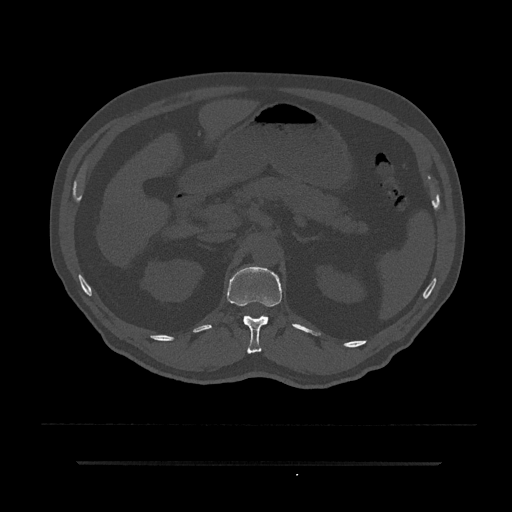
CT including the spine, one axial slice. Position 193 of 797 along the scan axis. Reconstruction kernel Br40s/3. Bone window (W 1800 / L 400 HU). 0.5 mm slice thickness. 512 × 512 image matrix, field of view 464 × 464 mm. Patient: male, 59 years. From the clinical record (not read from this slice): primary cancer: bile ducts; vertebrae with lytic lesions (as recorded): T10.
Structures marked on this image (semi-automatic segmentation, software-assisted and operator-edited):
- T12 vertebra: bounding box <227,266,282,354> (left, top, right, bottom; pixels)